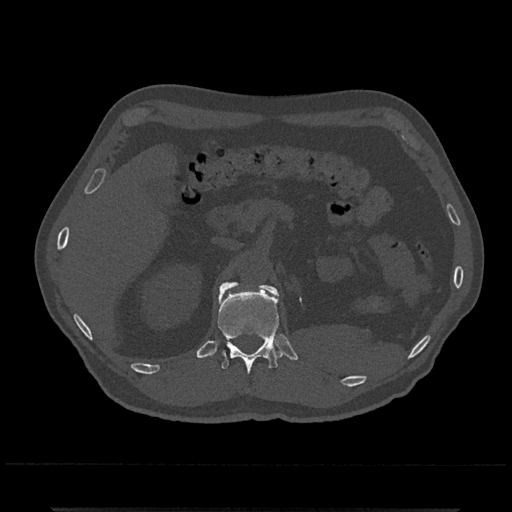
CT including the spine, one axial slice. Slice 422 of 797 in the series (ordered by position). Reconstruction kernel Br40s/3. 120 kVp. Bone window (W 1800 / L 400 HU). 0.5 mm slice thickness. 512 × 512 image matrix. Patient: male, 67 years. Case-level facts recorded for this patient, not image findings: primary cancer: prostate.
Structures marked on this image (semi-automatically segmented with operator editing):
- L1 vertebra: bounding box <258,283,277,295> (left, top, right, bottom; pixels)
- T12 vertebra: <217,282,282,374>